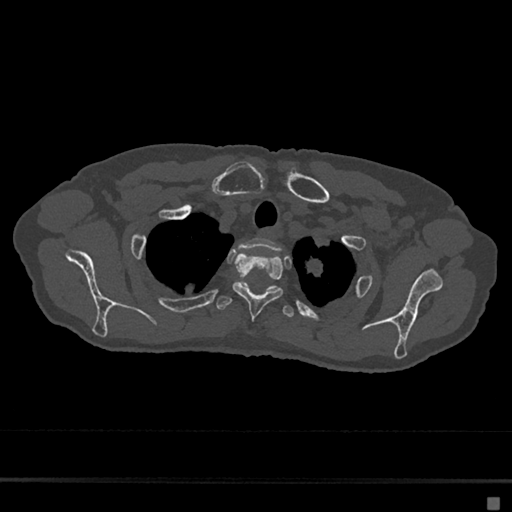
CT including the spine, one axial slice. Slice 569 of 797 in the series (ordered by position). Reconstruction kernel Br40s/3. Bone window (W 1800 / L 400 HU). 0.5 mm slice thickness. 512 × 512 image matrix. Patient: female, 68 years. Case-level facts recorded for this patient, not image findings: primary cancer: renal.
Annotated regions visible in this slice (semi-automatic segmentation, software-assisted and operator-edited):
- T1 vertebra: bounding box [x1, y1, x2, y2] px = [239, 238, 280, 252]
- T2 vertebra: [232, 253, 283, 318]
- T3 vertebra: [216, 281, 295, 317]